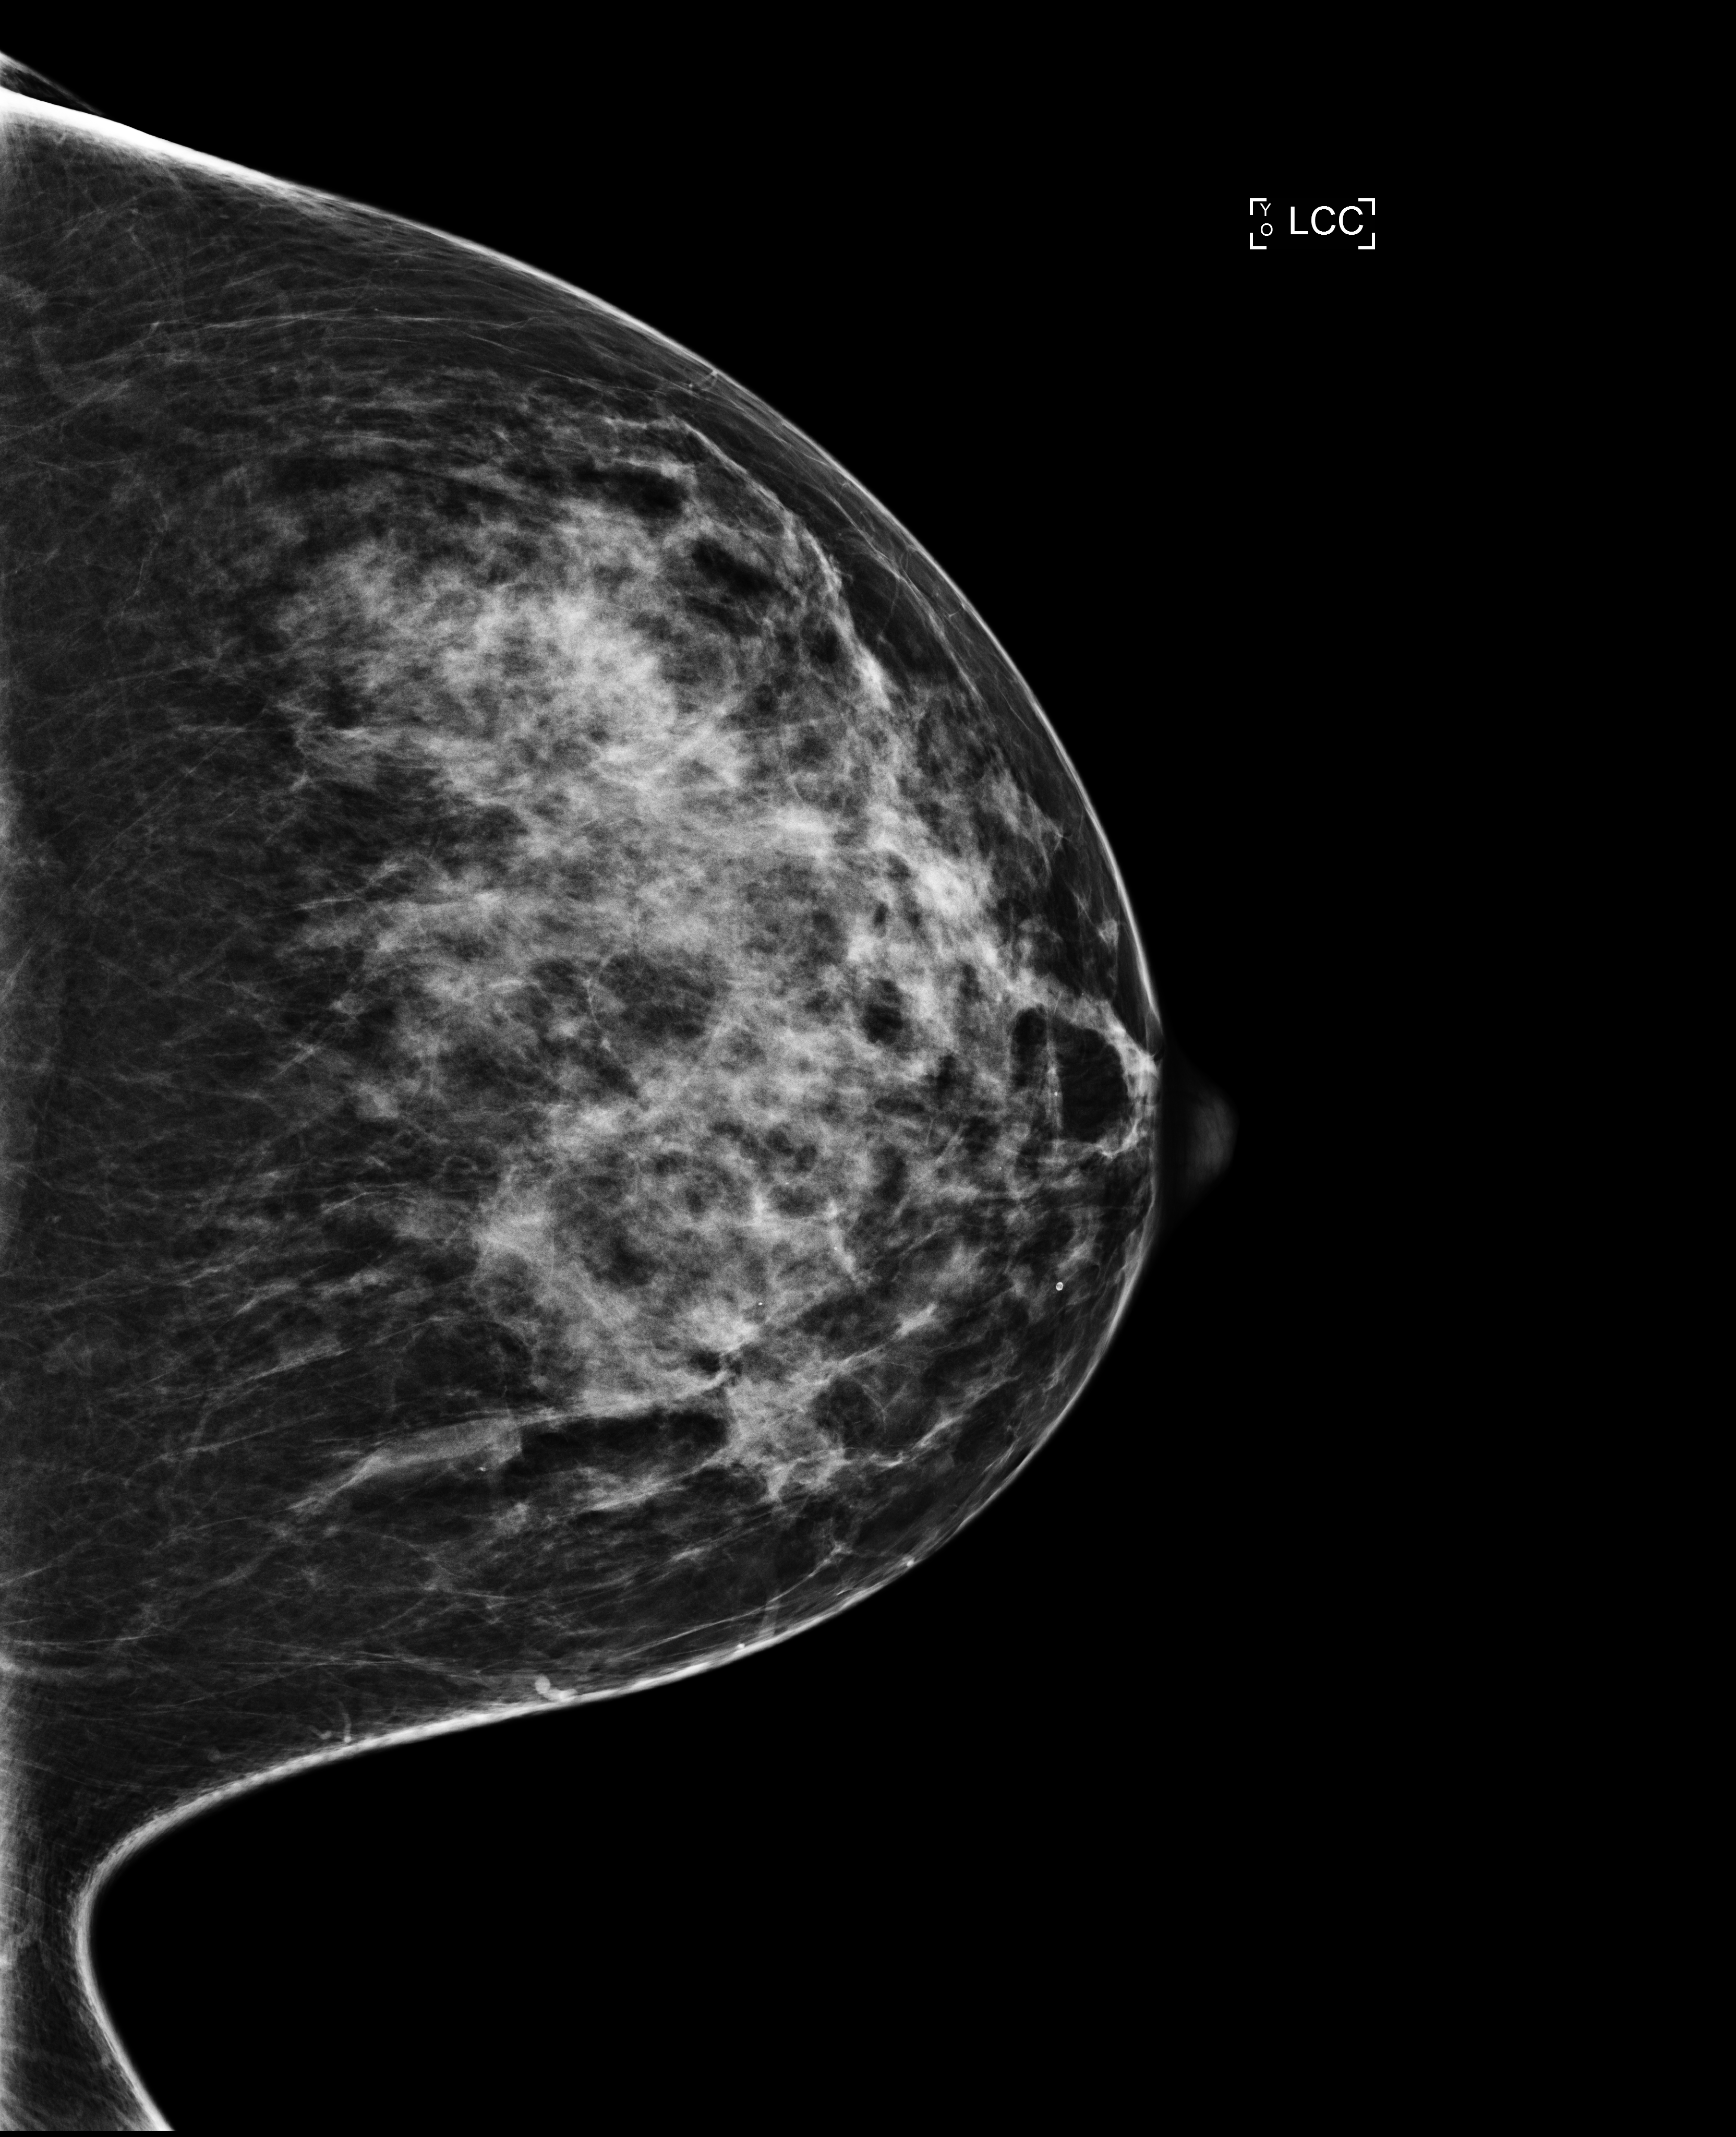
Digital mammogram (FFDM), left breast, CC view, annual screening mammography examination, system: Selenia Dimensions. Female patient, age 45 years.
BI-RADS breast density category at the screening exam (both breasts, scale 1–4): 3. Final BI-RADS assessment for this screening round (tomosynthesis exam, both breasts): category 2. Recall: no recall after this screen.